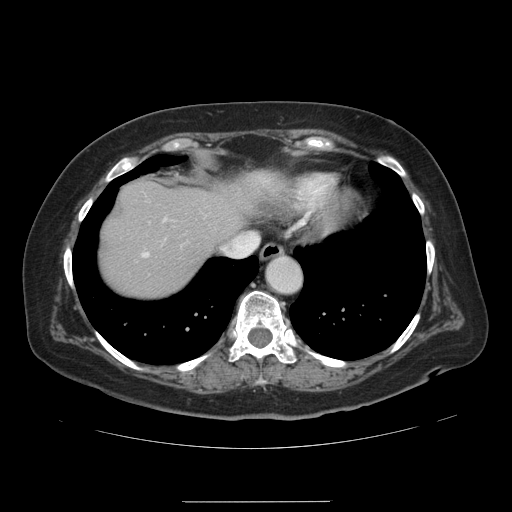
Contrast-enhanced abdominal CT, one axial slice; position 119 of 141 along the scan axis; intravenous contrast given; soft-tissue window (W 400 / L 40 HU); 2.5 mm slice thickness; 512 × 512 image matrix, field of view 393 × 393 mm. Female patient, age 74 years. From the clinical record (not read from this slice): diagnosis: colorectal cancer liver metastases, imaged before liver resection.
Annotated regions visible in this slice (expert manual segmentation):
- hepatic veins: bounding box (x1, y1, x2, y2) in pixels: (221, 234, 248, 250)
- liver: (102, 178, 269, 295)
- planned liver remnant (the part of the liver to remain after resection): (102, 178, 269, 287)